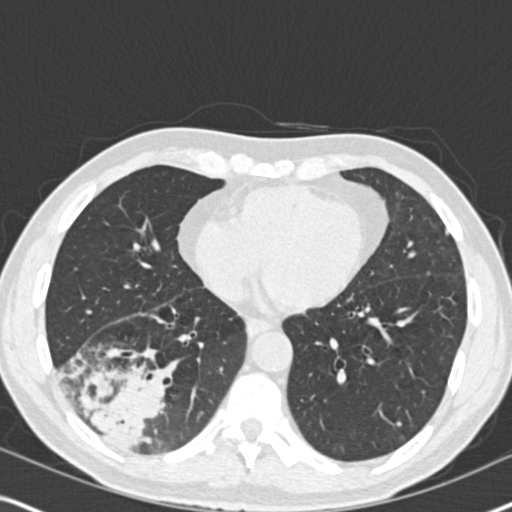
Low-dose screening chest CT, axial slice. Second screening round (one year after baseline). Lung window (W 1500 / L -600 HU). 2 mm slice thickness. Male, age 61 years at enrolment. Current smoker at enrolment.
Expert reader's lesion annotation, box from (x=50, y=326) to (x=189, y=464) px. Reader record for this screening exam (exam-level; its link to the box is not recorded): non-calcified nodule or mass ≥4 mm, right lower lobe, 90 × 80 mm, soft tissue attenuation, pre-existing on the prior screen: yes; interval growth: yes. Official screen result: positive, other. Participant outcome: lung cancer diagnosed 20 days after this screen — bronchiolo-alveolar adenocarcinoma, NOS, right lower lobe, moderately differentiated (G2), stage IIIB (AJCC 6th edition), 90 mm at pathology.